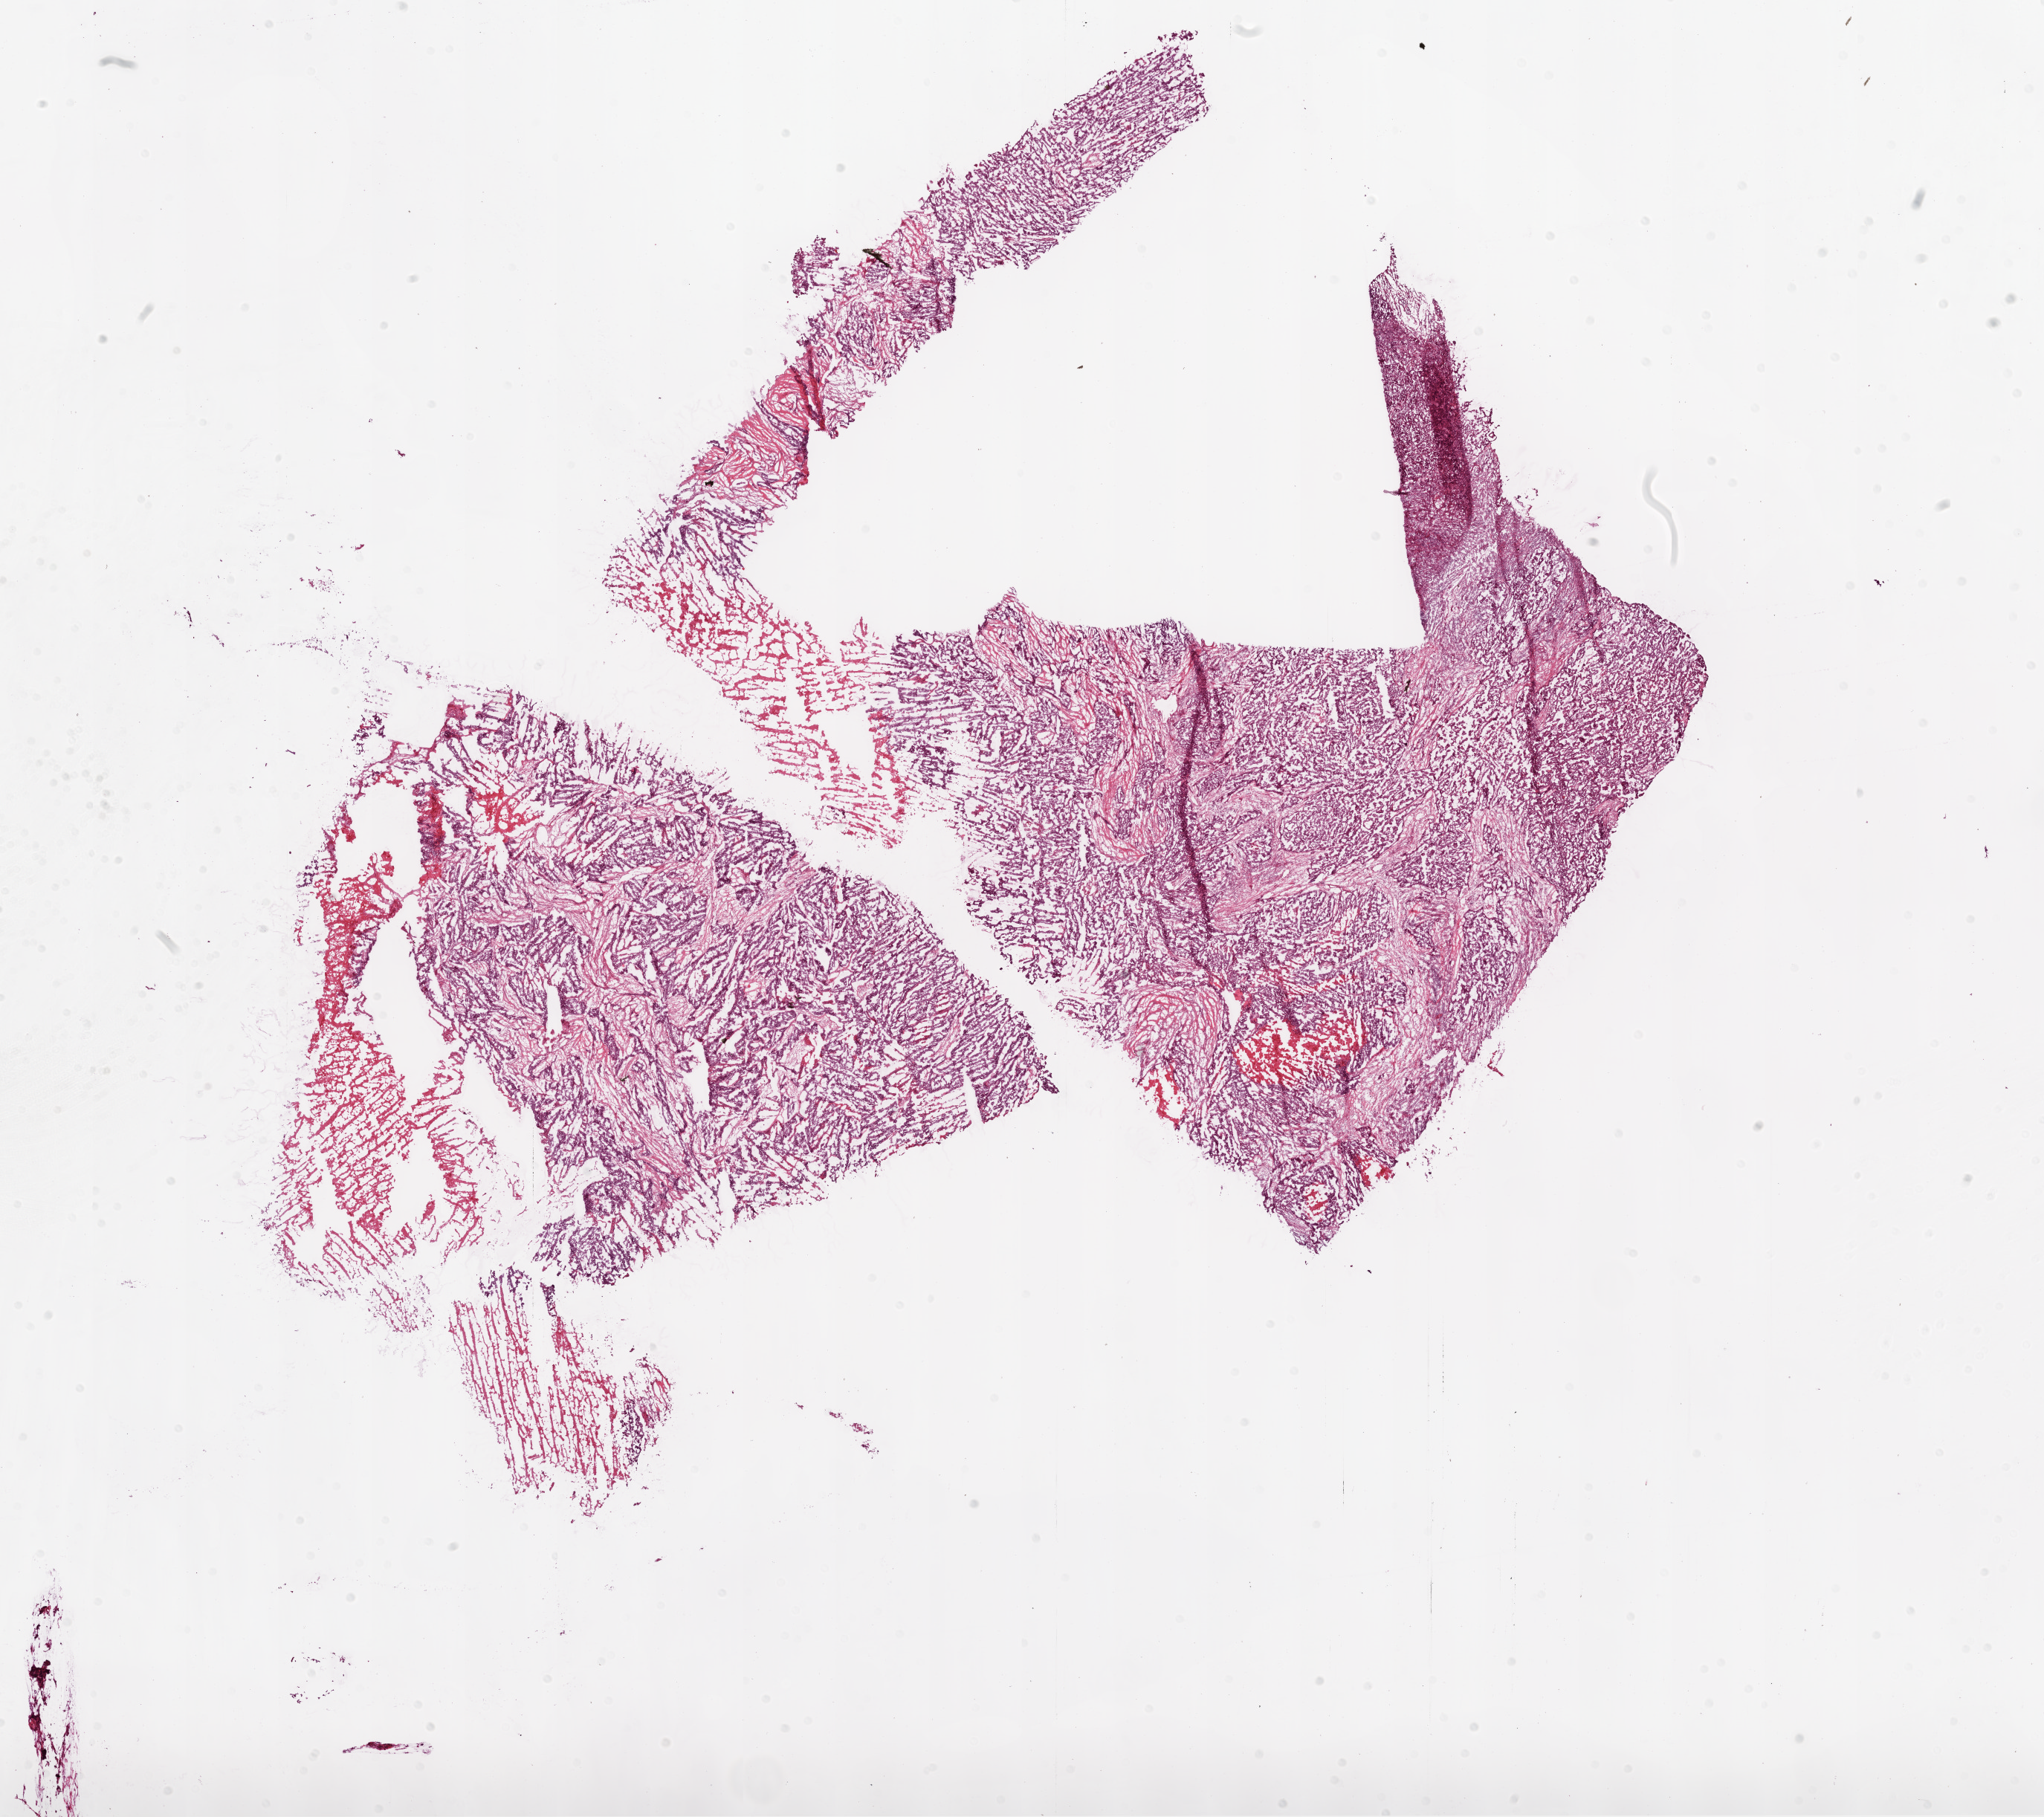
Whole-slide histology image, H&E-stained — a low-resolution overview of the entire scanned area, about 22.1 x 19.6 mm, frozen section from the bottom of the tissue portion, recurrent tumour sample from the ovary. Female patient; age at initial diagnosis 53 years. Composition of this section per pathologist review: tumour cells 70%, tumour nuclei 70%, normal cells 0%, stromal cells 20%, necrosis 10%.
- this section: recurrent tumour
- patient diagnosis: Serous cystadenocarcinoma, NOS